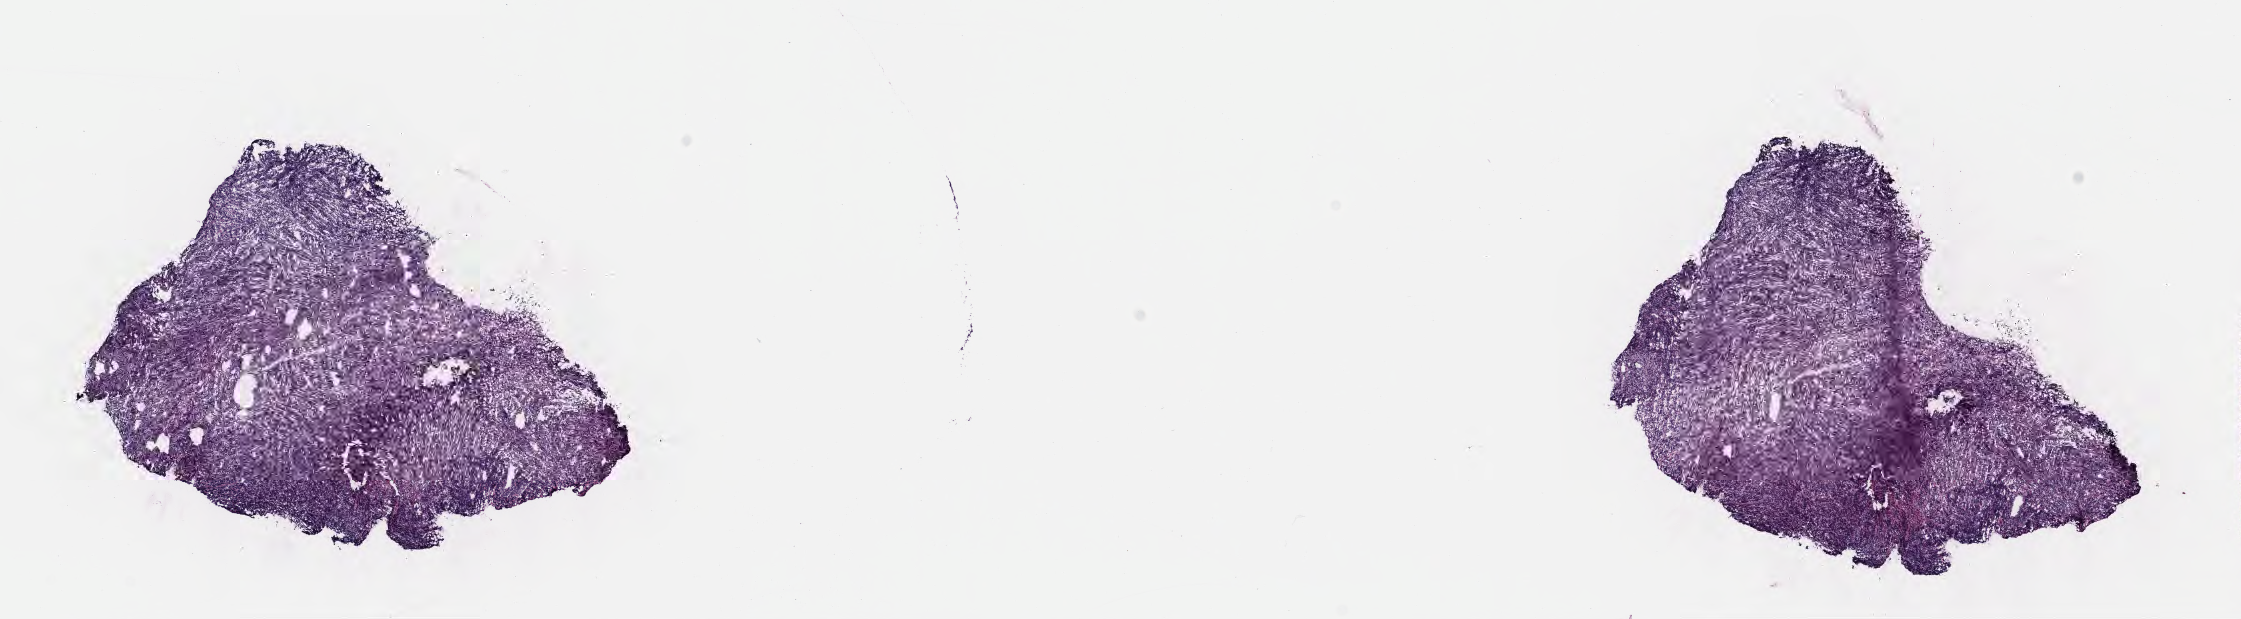
H&E whole-slide image — shown as a low-resolution overview of the whole scanned area (about 18.1 x 5.0 mm). Frozen section (tissue freezing medium). Specimen: primary tumor. Site: cranium. Male patient; age at initial diagnosis 6 years. Pathologist review of this section (percent, as recorded): tumor cells 95%, tumor nuclei 90%, stromal cells 0%, necrosis 5%, normal cells 0%. Infiltration values recorded for this section: lymphocyte infiltration 40%, monocyte infiltration 20%, neutrophil infiltration 5%.
Diagnosis: Burkitt lymphoma, NOS. Section: top of the tissue portion. Ann Arbor stage (patient): Stage III.